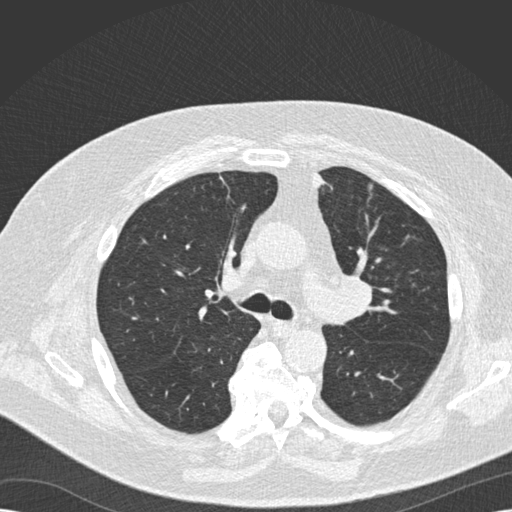
Low-dose screening chest CT, one axial slice. Position 110 of 173 along the scan axis. 120 kVp. Lung window (W 1500 / L -600 HU). 512 × 512 image matrix.
Structures marked on this image (outlined manually by an expert reader):
- lesion 1 (tumor, upper lobe of left lung): box from (x=314, y=172) to (x=324, y=188) px